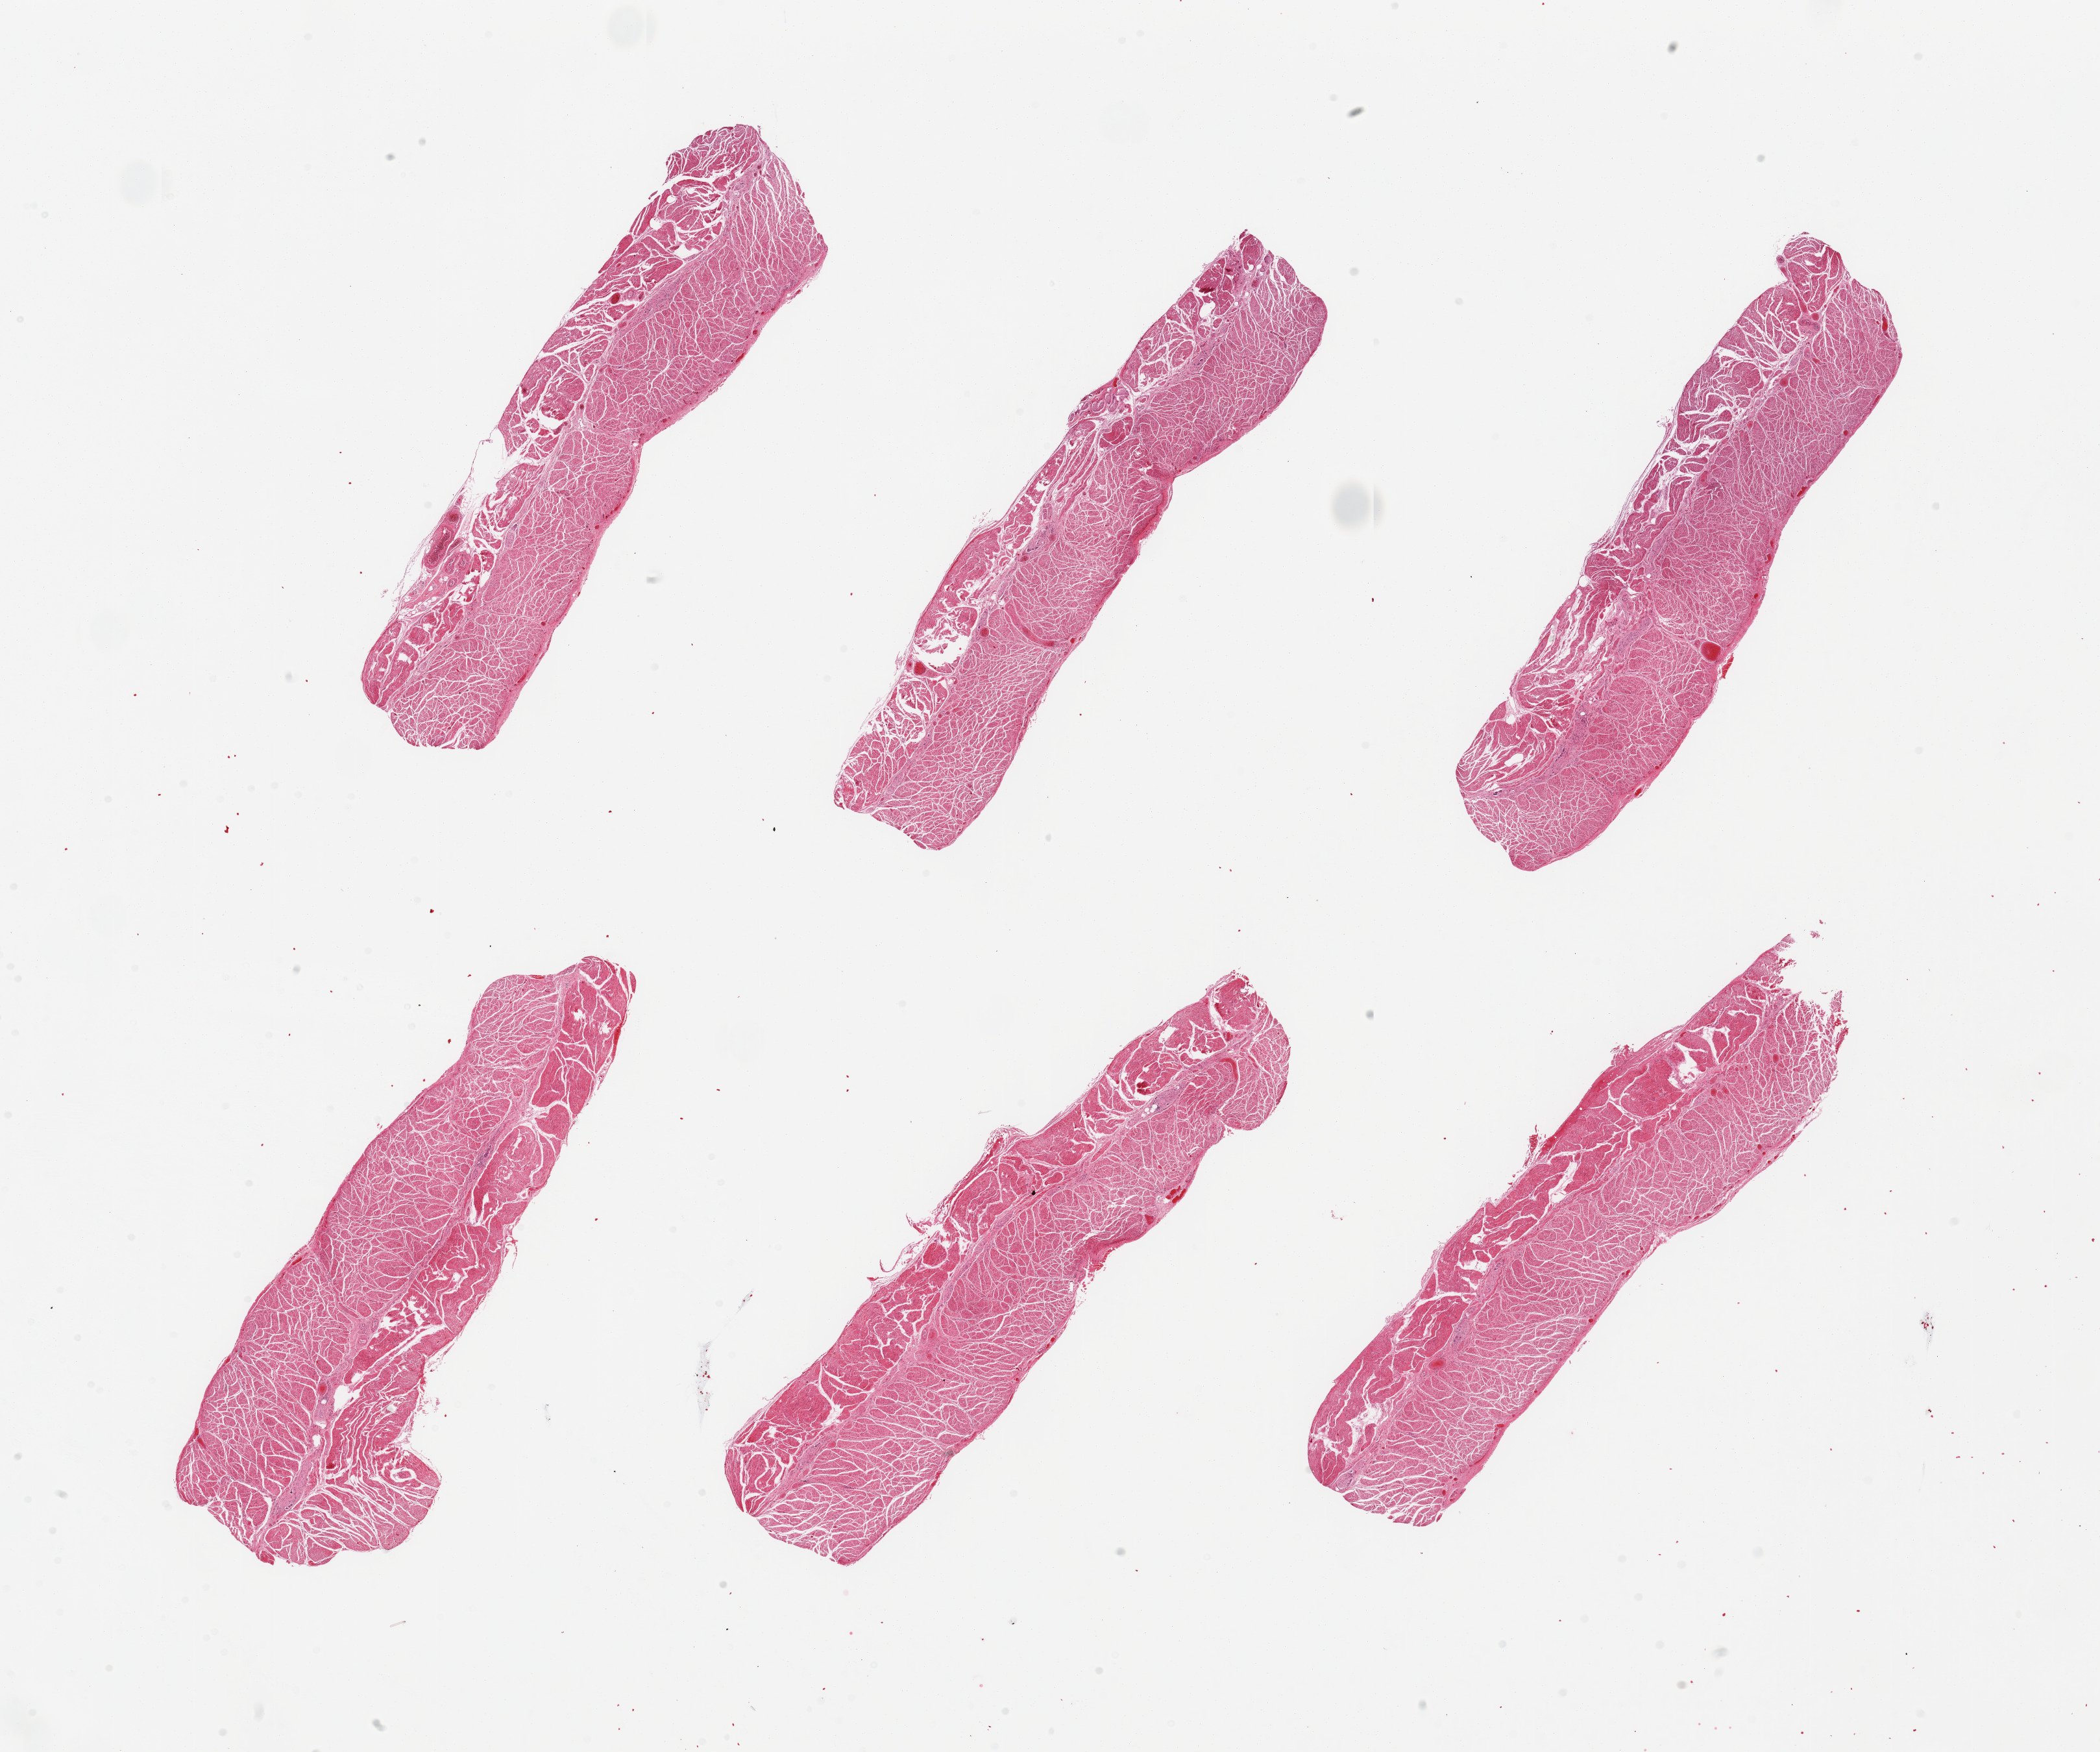
Whole-slide image, haematoxylin and eosin stain — a low-resolution overview of the entire scanned area, about 25.6 x 21.3 mm (slide scanned at 20x). PAXgene-fixed paraffin-embedded (PFPE) section. Section of gastroesophageal junction (target tissue). Donor tissue sample. Donor: male.
Pathologist's review note for this sample: 6 pieces; well trimmed.